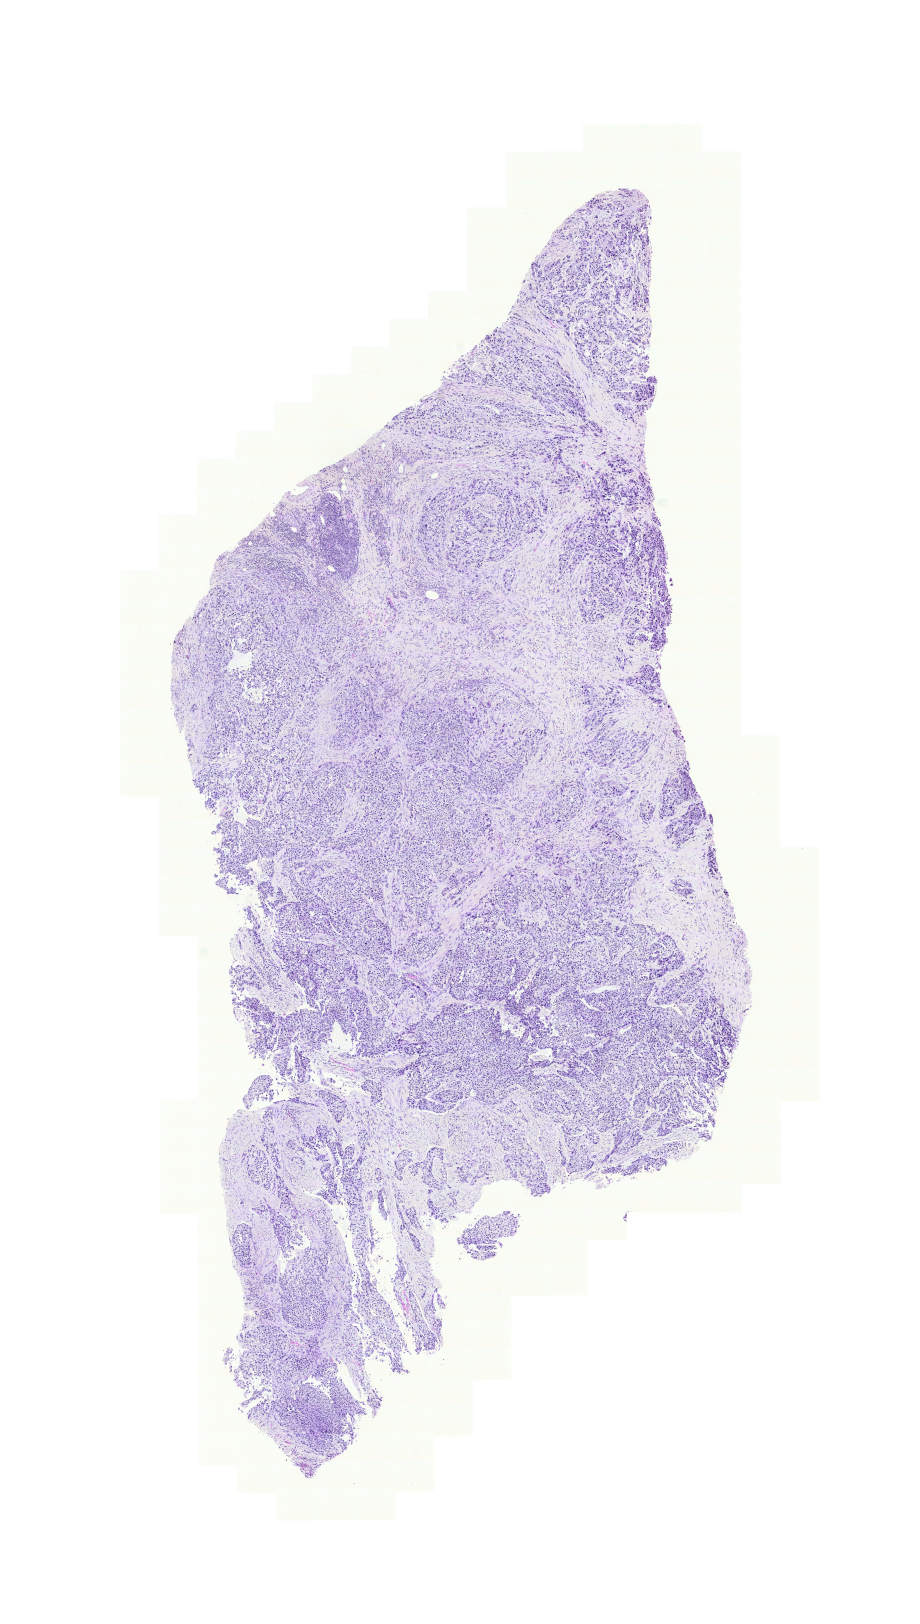
Hematoxylin and eosin (H&E) stained whole-slide image — low-resolution overview of the scanned area, about 6.8 x 12.1 mm (acquisition: 20x scan), FFPE section, primary tumour sample from the bladder. Female patient; age at initial diagnosis 82 years. Histologic grade: high grade.
• histologic diagnosis: Transitional cell carcinoma
• AJCC pathologic stage: III